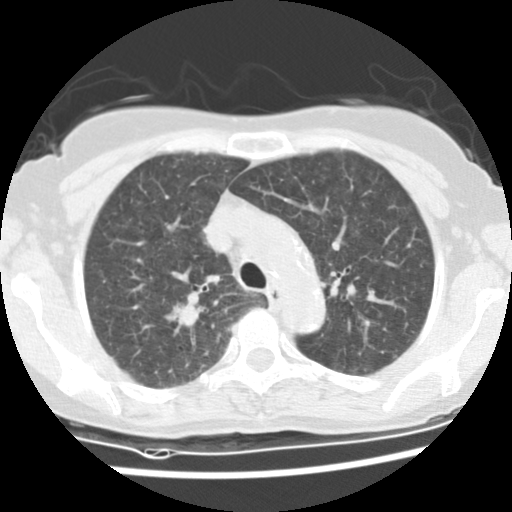
Low-dose screening chest CT, one axial slice. Slice 102 of 134 in the series (ordered by position). 120 kVp. Lung window (W 1500 / L -600 HU). 512 × 512 image matrix, field of view 298 × 298 mm.
Structures marked on this image (outlined manually by an expert reader):
- lesion 1 (tumor, upper lobe of right lung): bounding box [x1, y1, x2, y2] px = [164, 303, 201, 332]